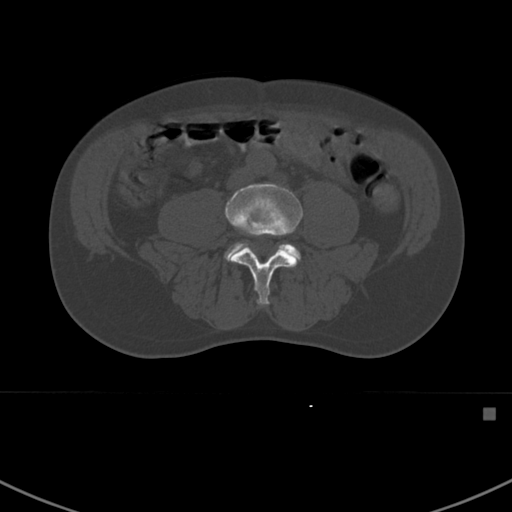
CT including the spine, one axial slice. Position 235 of 412 along the scan axis. Reconstruction kernel Br40s. Bone window (W 1800 / L 400 HU). 1.5 mm slice thickness. 512 × 512 image matrix. Patient: male, 59 years. From the clinical record (not read from this slice): primary cancer: prostate.
Outlined on this slice (semi-automatic segmentation, software-assisted and operator-edited):
- L4 vertebra: box from (x=225, y=183) to (x=303, y=306) px
- L5 vertebra: (x=225, y=243)–(x=301, y=262)